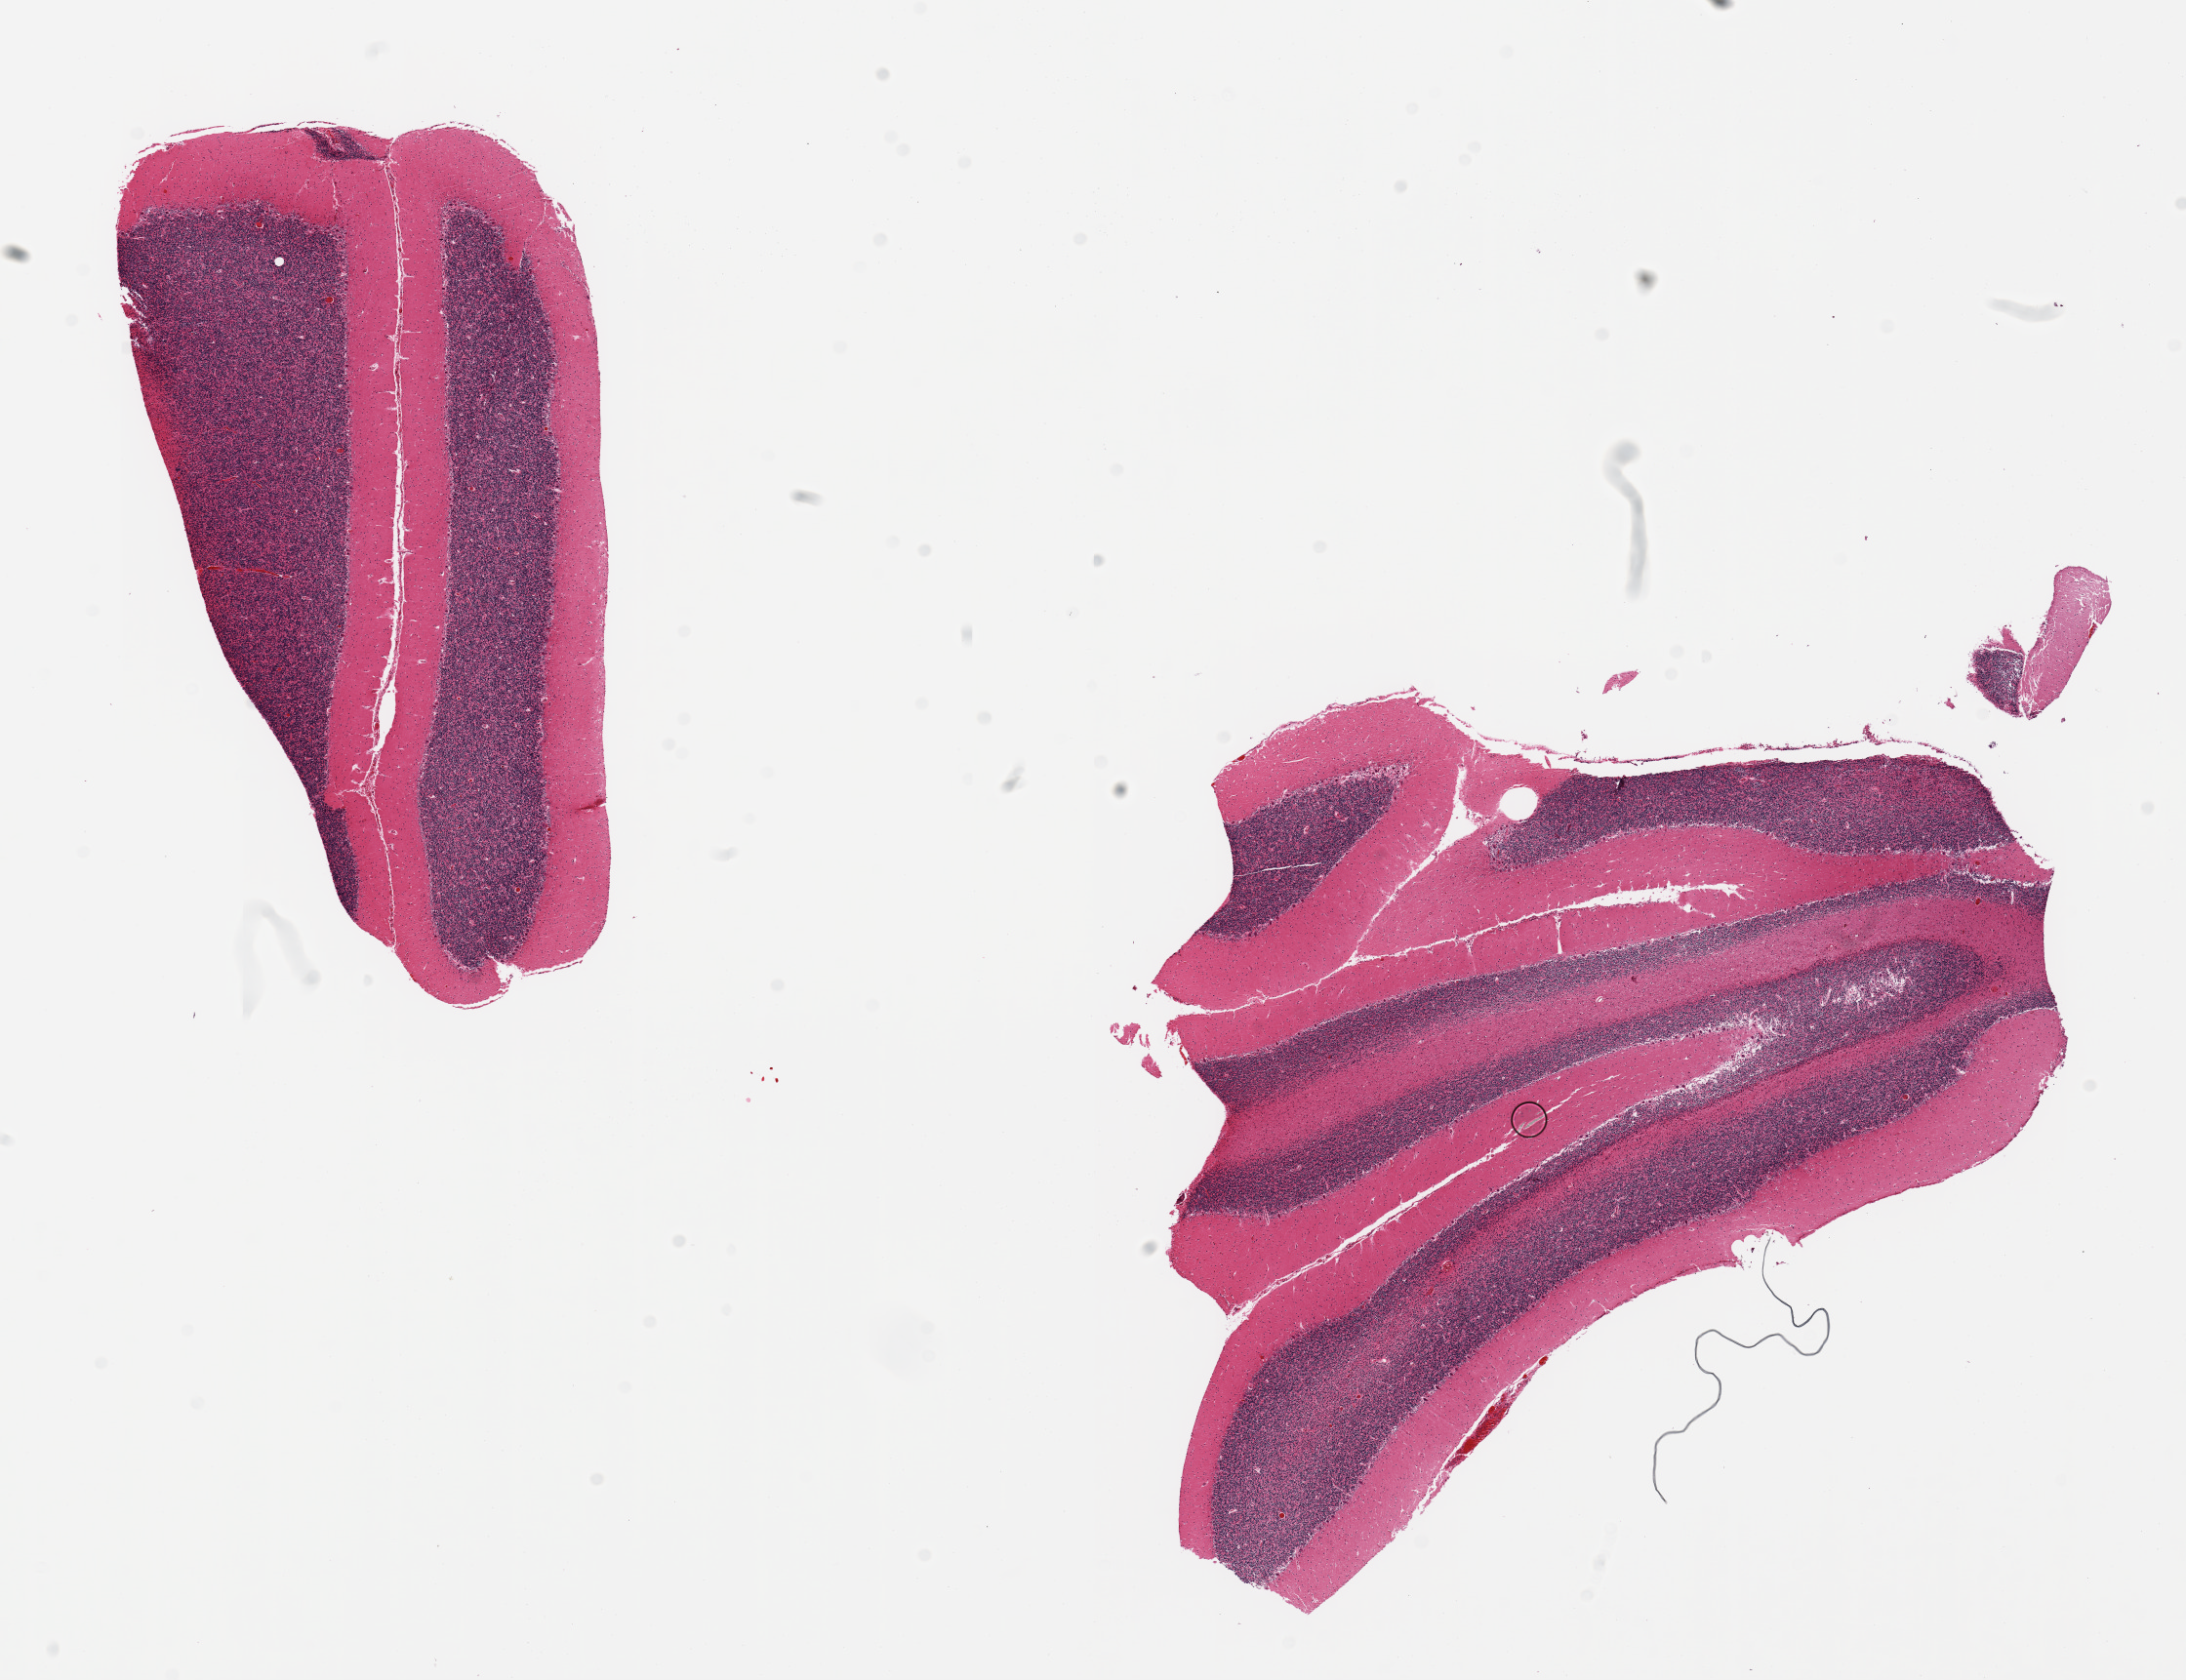
Whole-slide image, H&E stain — shown as a low-resolution overview of the whole scanned area (about 17.7 x 13.6 mm, acquisition: 20x scan); PAXgene-fixed paraffin-embedded (PFPE) section; section of cerebellum (target tissue); donor tissue sample. Donor sex: male.
Reviewer comment on this tissue sample: 2 pieces.